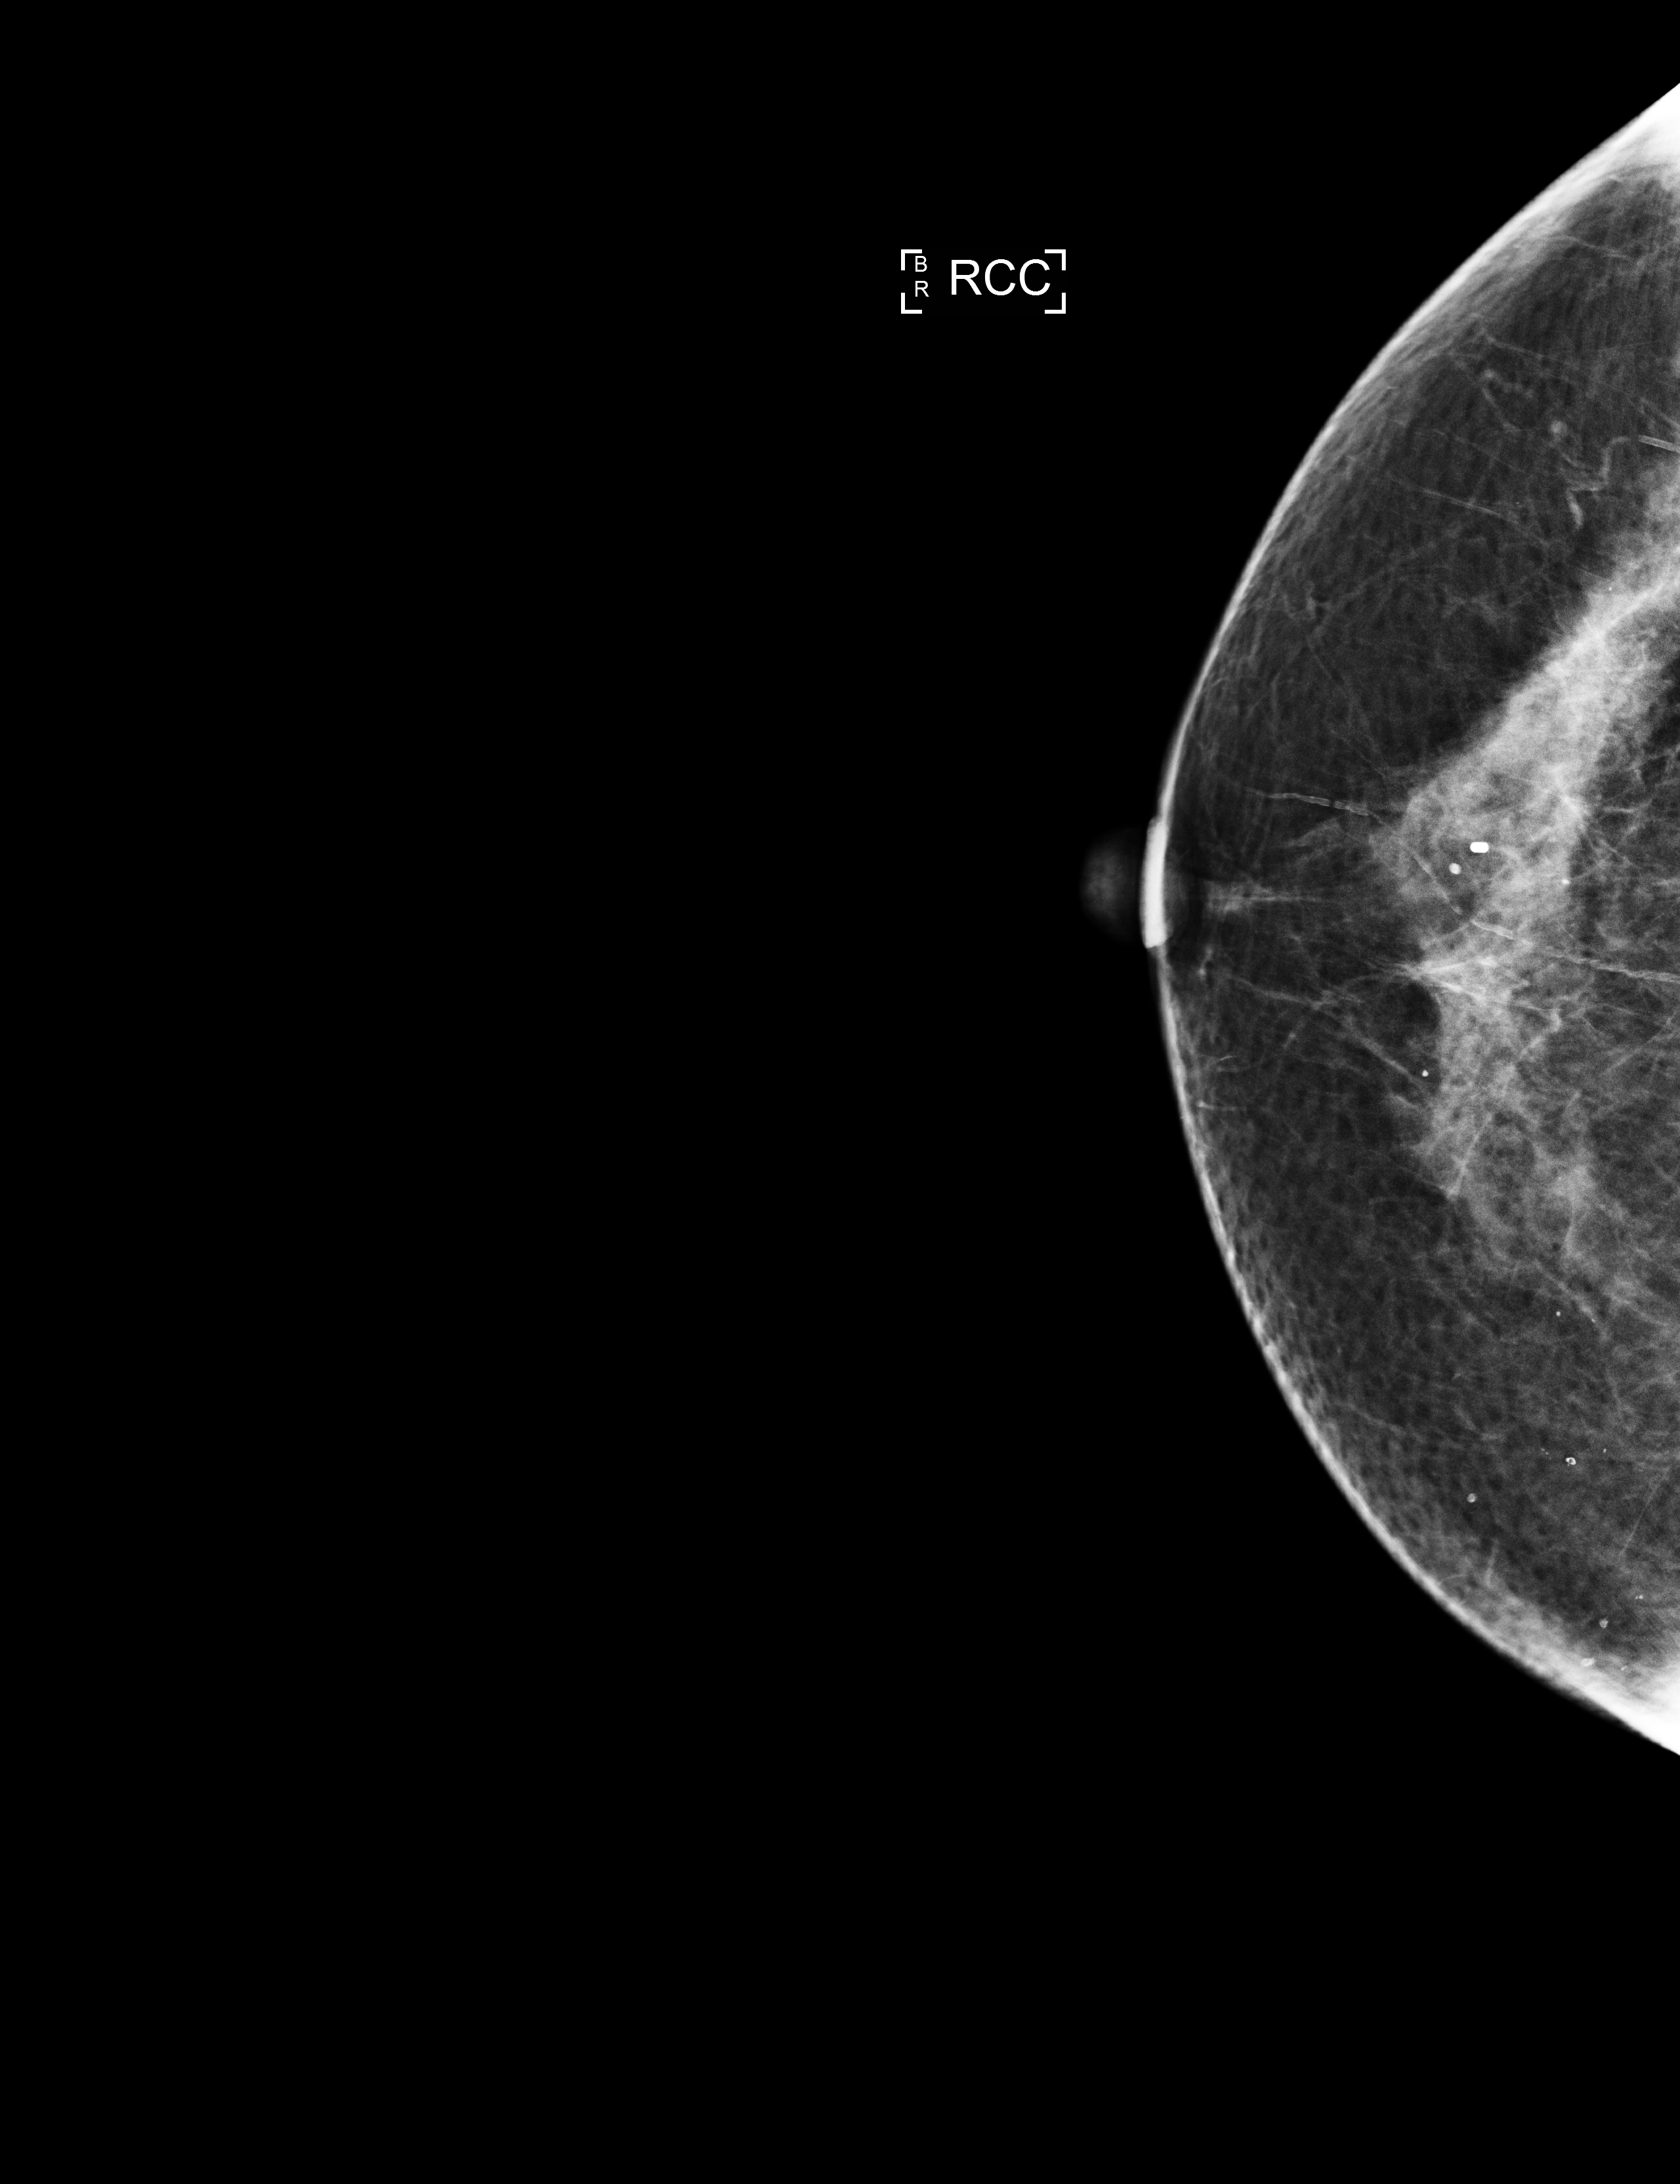
Screening examination. Patient aged 69 years (female).
Image type: full-field digital mammogram. Breast: right. Projection: CC view.